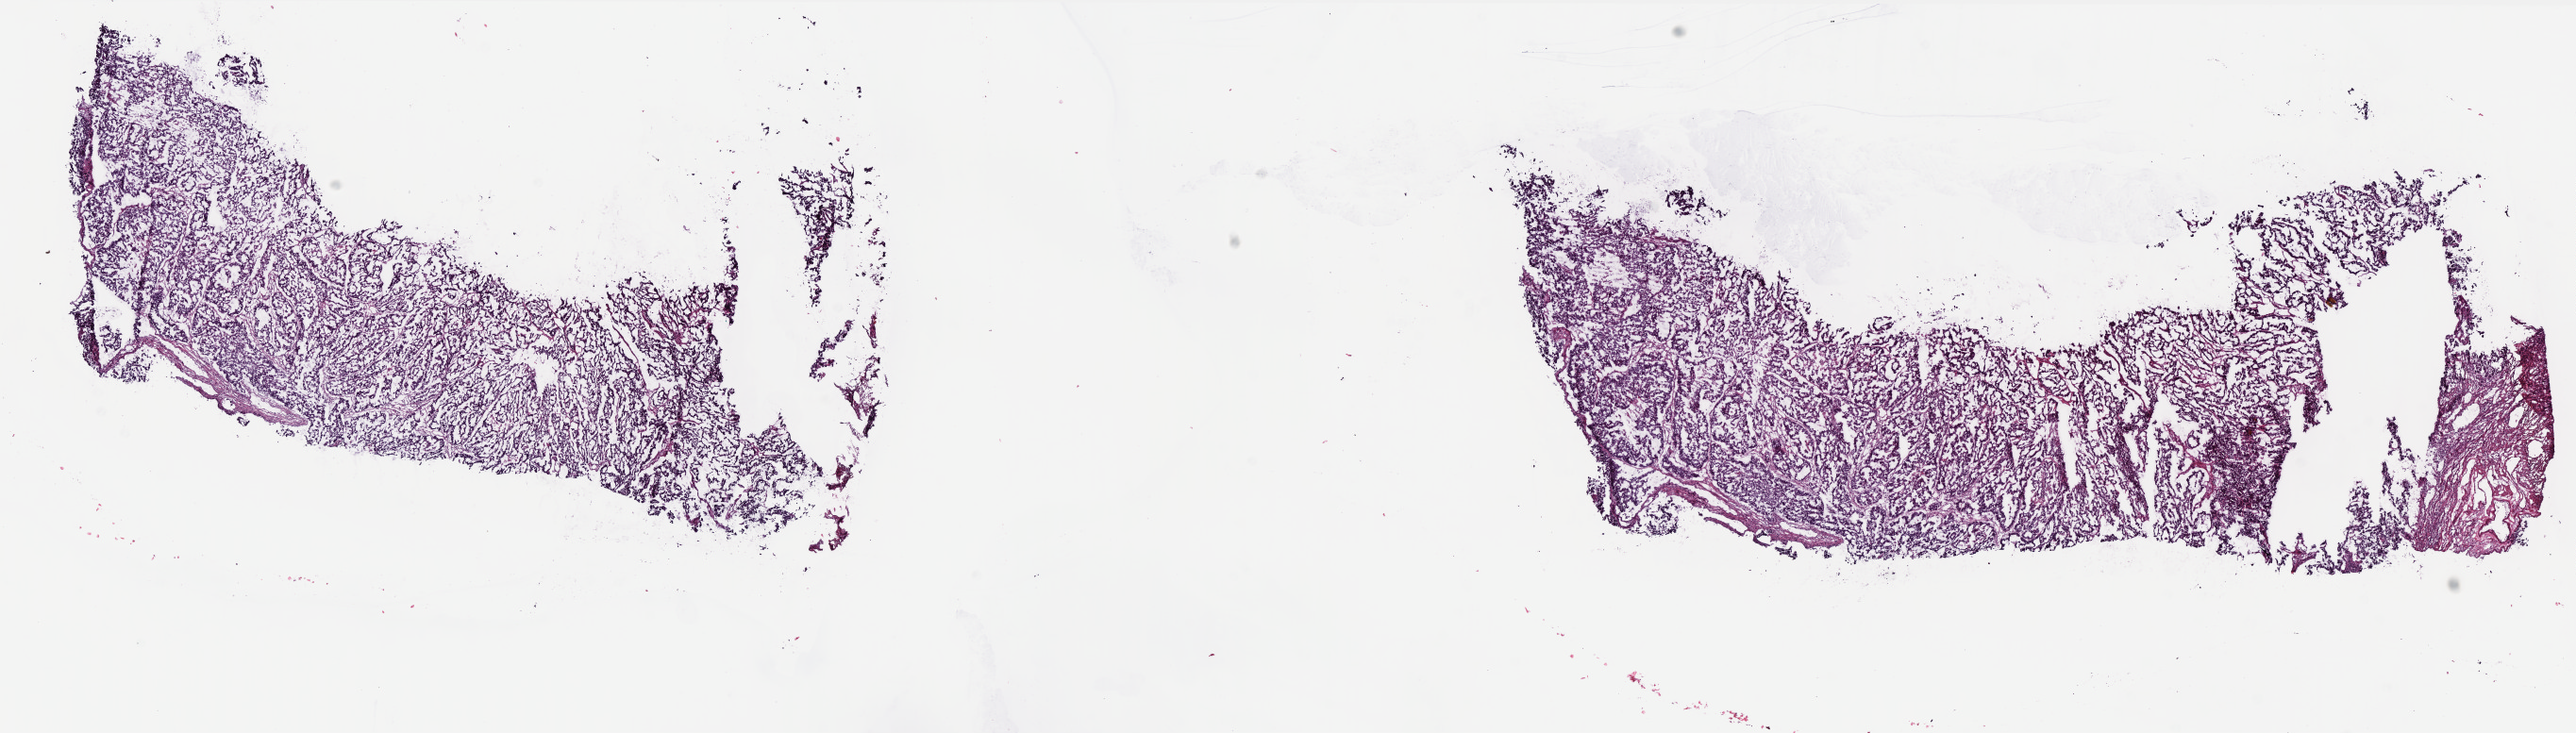
Whole-slide histology image, Hematoxylin and eosin (H&E) stained — low-resolution overview of the scanned area, about 21.9 x 6.2 mm (slide scanned at 40x); frozen section; uterus, primary tumour sample. Female, age 81 years at initial diagnosis. Histologic grade: G3 (poorly differentiated). Slide review estimates, as recorded: tumour cells 82%, tumour nuclei 90%, normal cells 10%, stromal cells 5%, necrosis 3%. Inflammatory infiltration, as recorded: lymphocyte infiltration 2%, monocyte infiltration 0%, neutrophil infiltration 0%.
• FIGO stage: II
• pathologic diagnosis: Serous cystadenocarcinoma, NOS (endometrium)